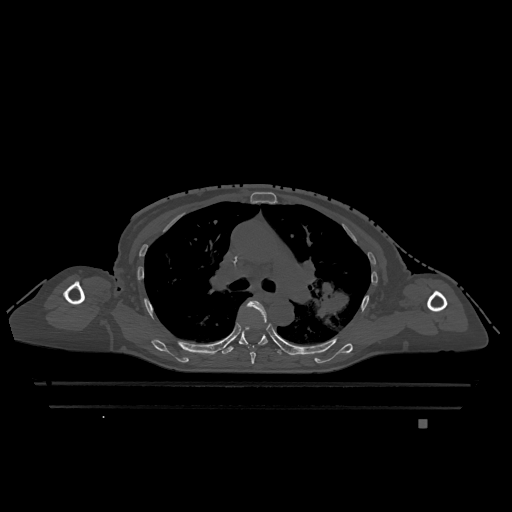
CT including the spine, one axial slice. Bone window (W 1800 / L 400 HU). 512 × 512 image matrix, field of view 500 × 500 mm. Patient: female, 74 years. Case-level facts recorded for this patient, not image findings: primary cancer: lung; vertebrae with lytic lesions (as recorded): T1, T4, T5, T6, L4, L5.
Outlined on this slice (semi-automatically segmented with operator editing):
- T5 vertebra: bounding box (x1, y1, x2, y2) in pixels: (243, 301, 267, 364)
- T6 vertebra: (222, 326, 281, 355)